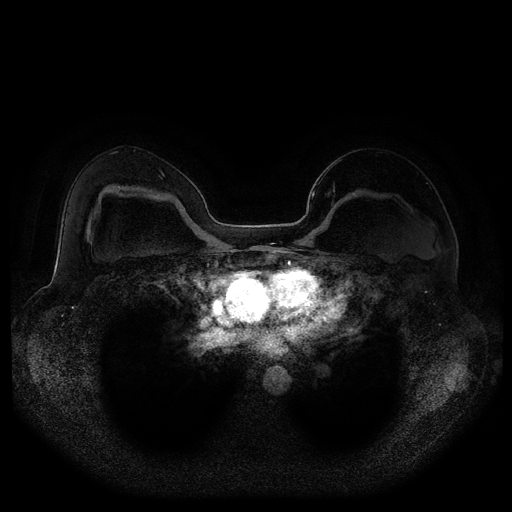
Breast MRI (dynamic contrast-enhanced, multi-phase), one axial slice; slice 68 of 116 in the series (ordered by position); dynamic contrast-enhanced series, time point 2 of 5 at this slice position (early post-contrast); 1.5 T; TE 2.5 ms, TR 5.2 ms; 2.1 mm slice thickness; 512 × 512 image matrix, field of view 380 × 380 mm. Female patient, age 43 years.
Outlined on this slice (semi-automatic segmentation, software-assisted and operator-edited):
- breast lesion (labelled benign in the annotation): box from (x=325, y=190) to (x=331, y=197) px